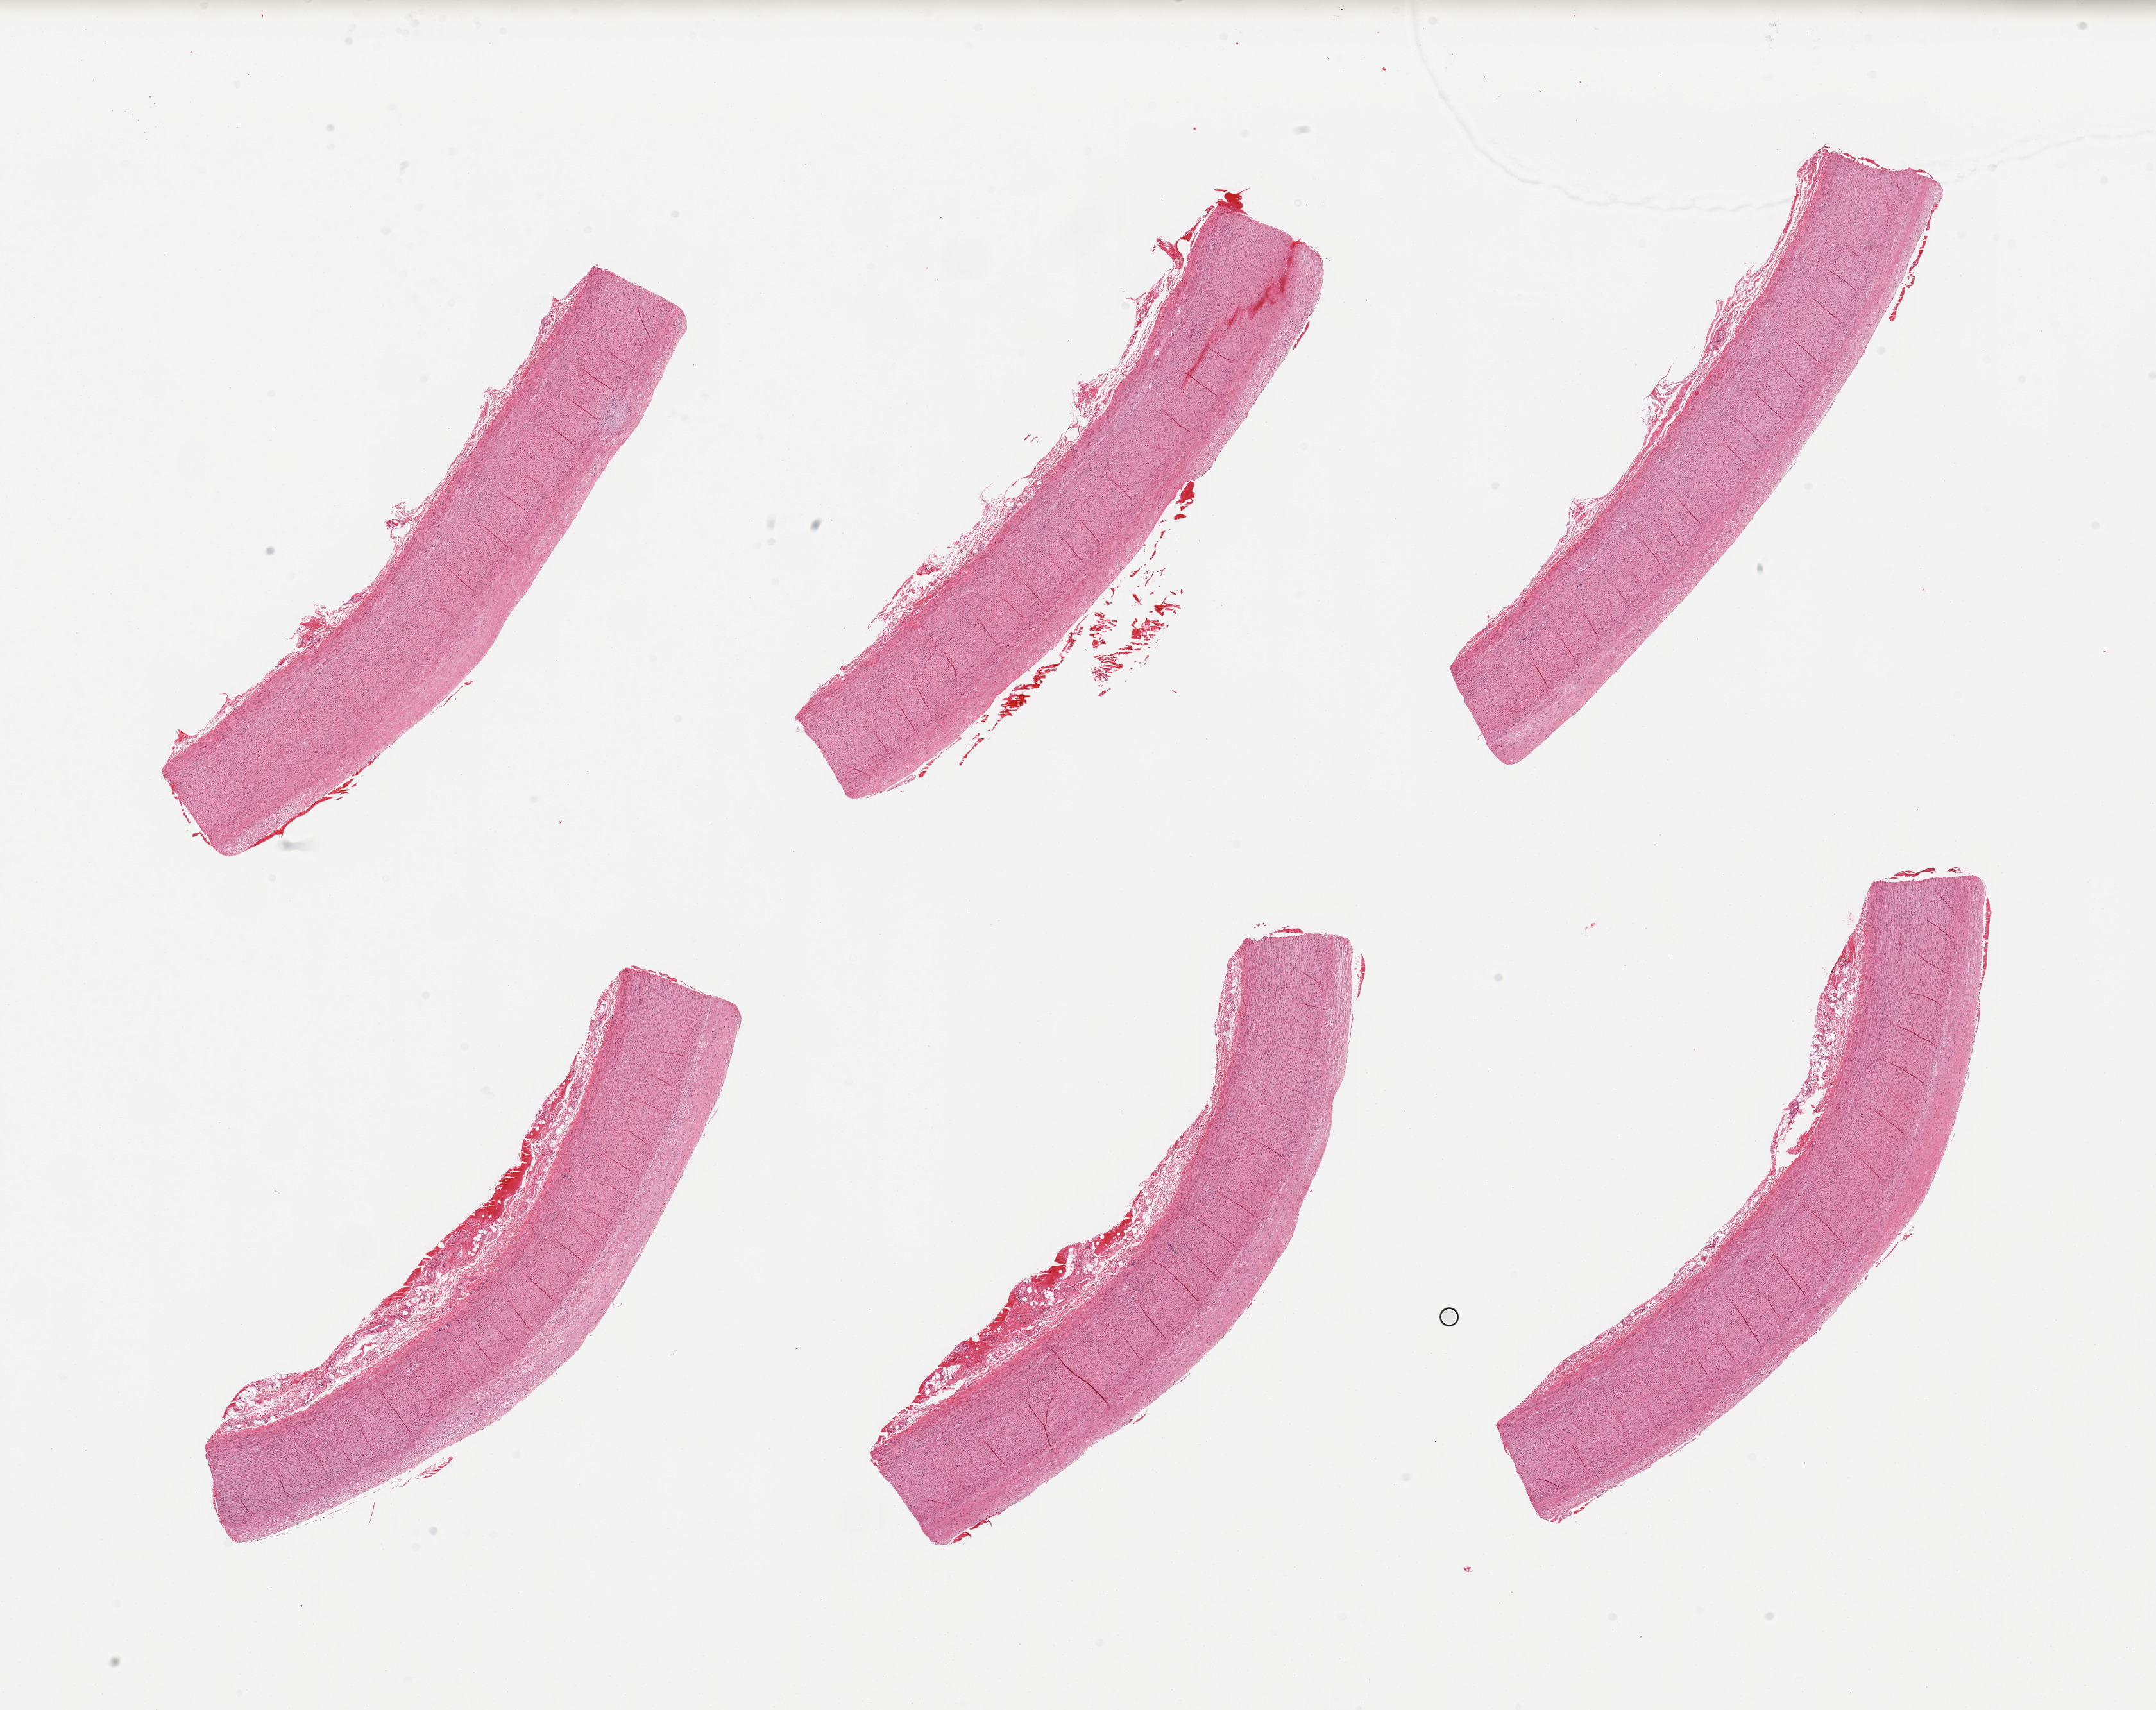
Whole-slide image, H&E stain, low-resolution overview of the scanned area, about 26.6 x 21.1 mm (from a 20x scan). PAXgene-fixed, paraffin-embedded tissue. Target tissue: aorta. Tissue donor sample. Donor sex: male.
Review note (as recorded): 6 pieces; atherosclerosis.